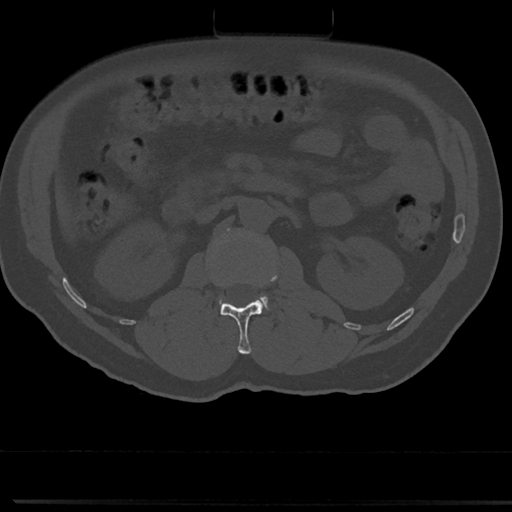
CT including the spine, one axial slice; position 54 of 817 along the scan axis; reconstruction kernel Br40s/3; 120 kVp; bone window (W 1800 / L 400 HU); 0.5 mm slice thickness; 512 × 512 image matrix. Patient: male, 61 years. Case-level facts recorded for this patient, not image findings: primary cancer: prostate.
Outlined on this slice (semi-automatically segmented with operator editing):
- L1 vertebra: box from (x=220, y=265) to (x=278, y=354) px
- L2 vertebra: (x=215, y=230)–(x=269, y=311)